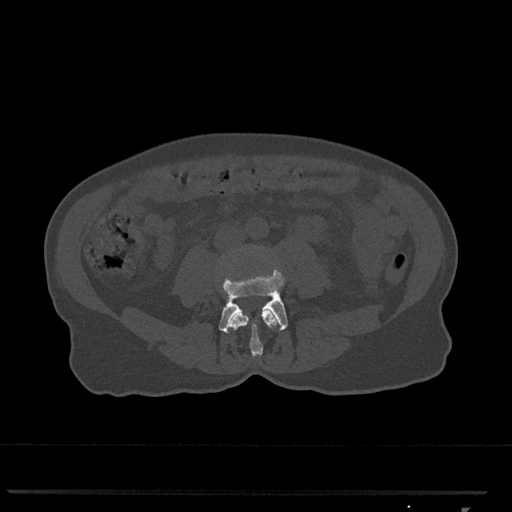
CT including the spine, one axial slice. Slice 234 of 793 in the series (ordered by position). Reconstruction kernel Br40s/3. 120 kVp. Bone window (W 1800 / L 400 HU). 0.5 mm slice thickness. 512 × 512 image matrix, field of view 380 × 380 mm. Female patient, age 62 years. From the clinical record (not read from this slice): primary cancer: renal.
Structures marked on this image (semi-automatic segmentation, software-assisted and operator-edited):
- L3 vertebra: bounding box (x1, y1, x2, y2) in pixels: (229, 309, 277, 357)
- L4 vertebra: (219, 269, 288, 333)